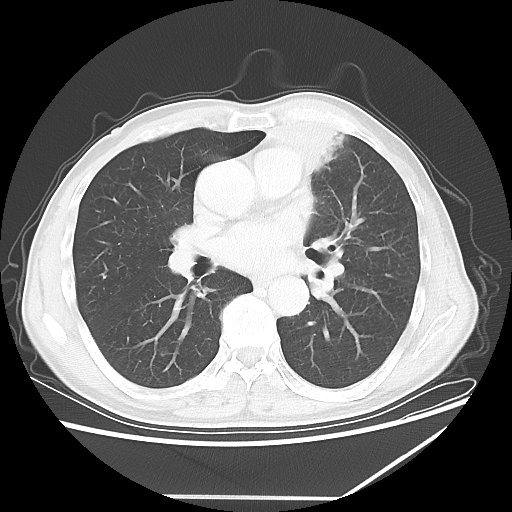
Chest CT, one axial slice. Position 32 of 64 along the scan axis. Reconstruction kernel LUNG. Lung window (W 1500 / L -600 HU). 5 mm slice thickness. 512 × 512 image matrix, field of view 383 × 383 mm. Male patient, age 64 years. Case-level facts recorded for this patient, not image findings: clinical TNM (as recorded): T1c N1 M1.
Annotated regions visible in this slice (bounding box drawn by a radiologist):
- lung tumour (recorded histology: squamous cell carcinoma): bounding box [x1, y1, x2, y2] px = [241, 77, 350, 184]